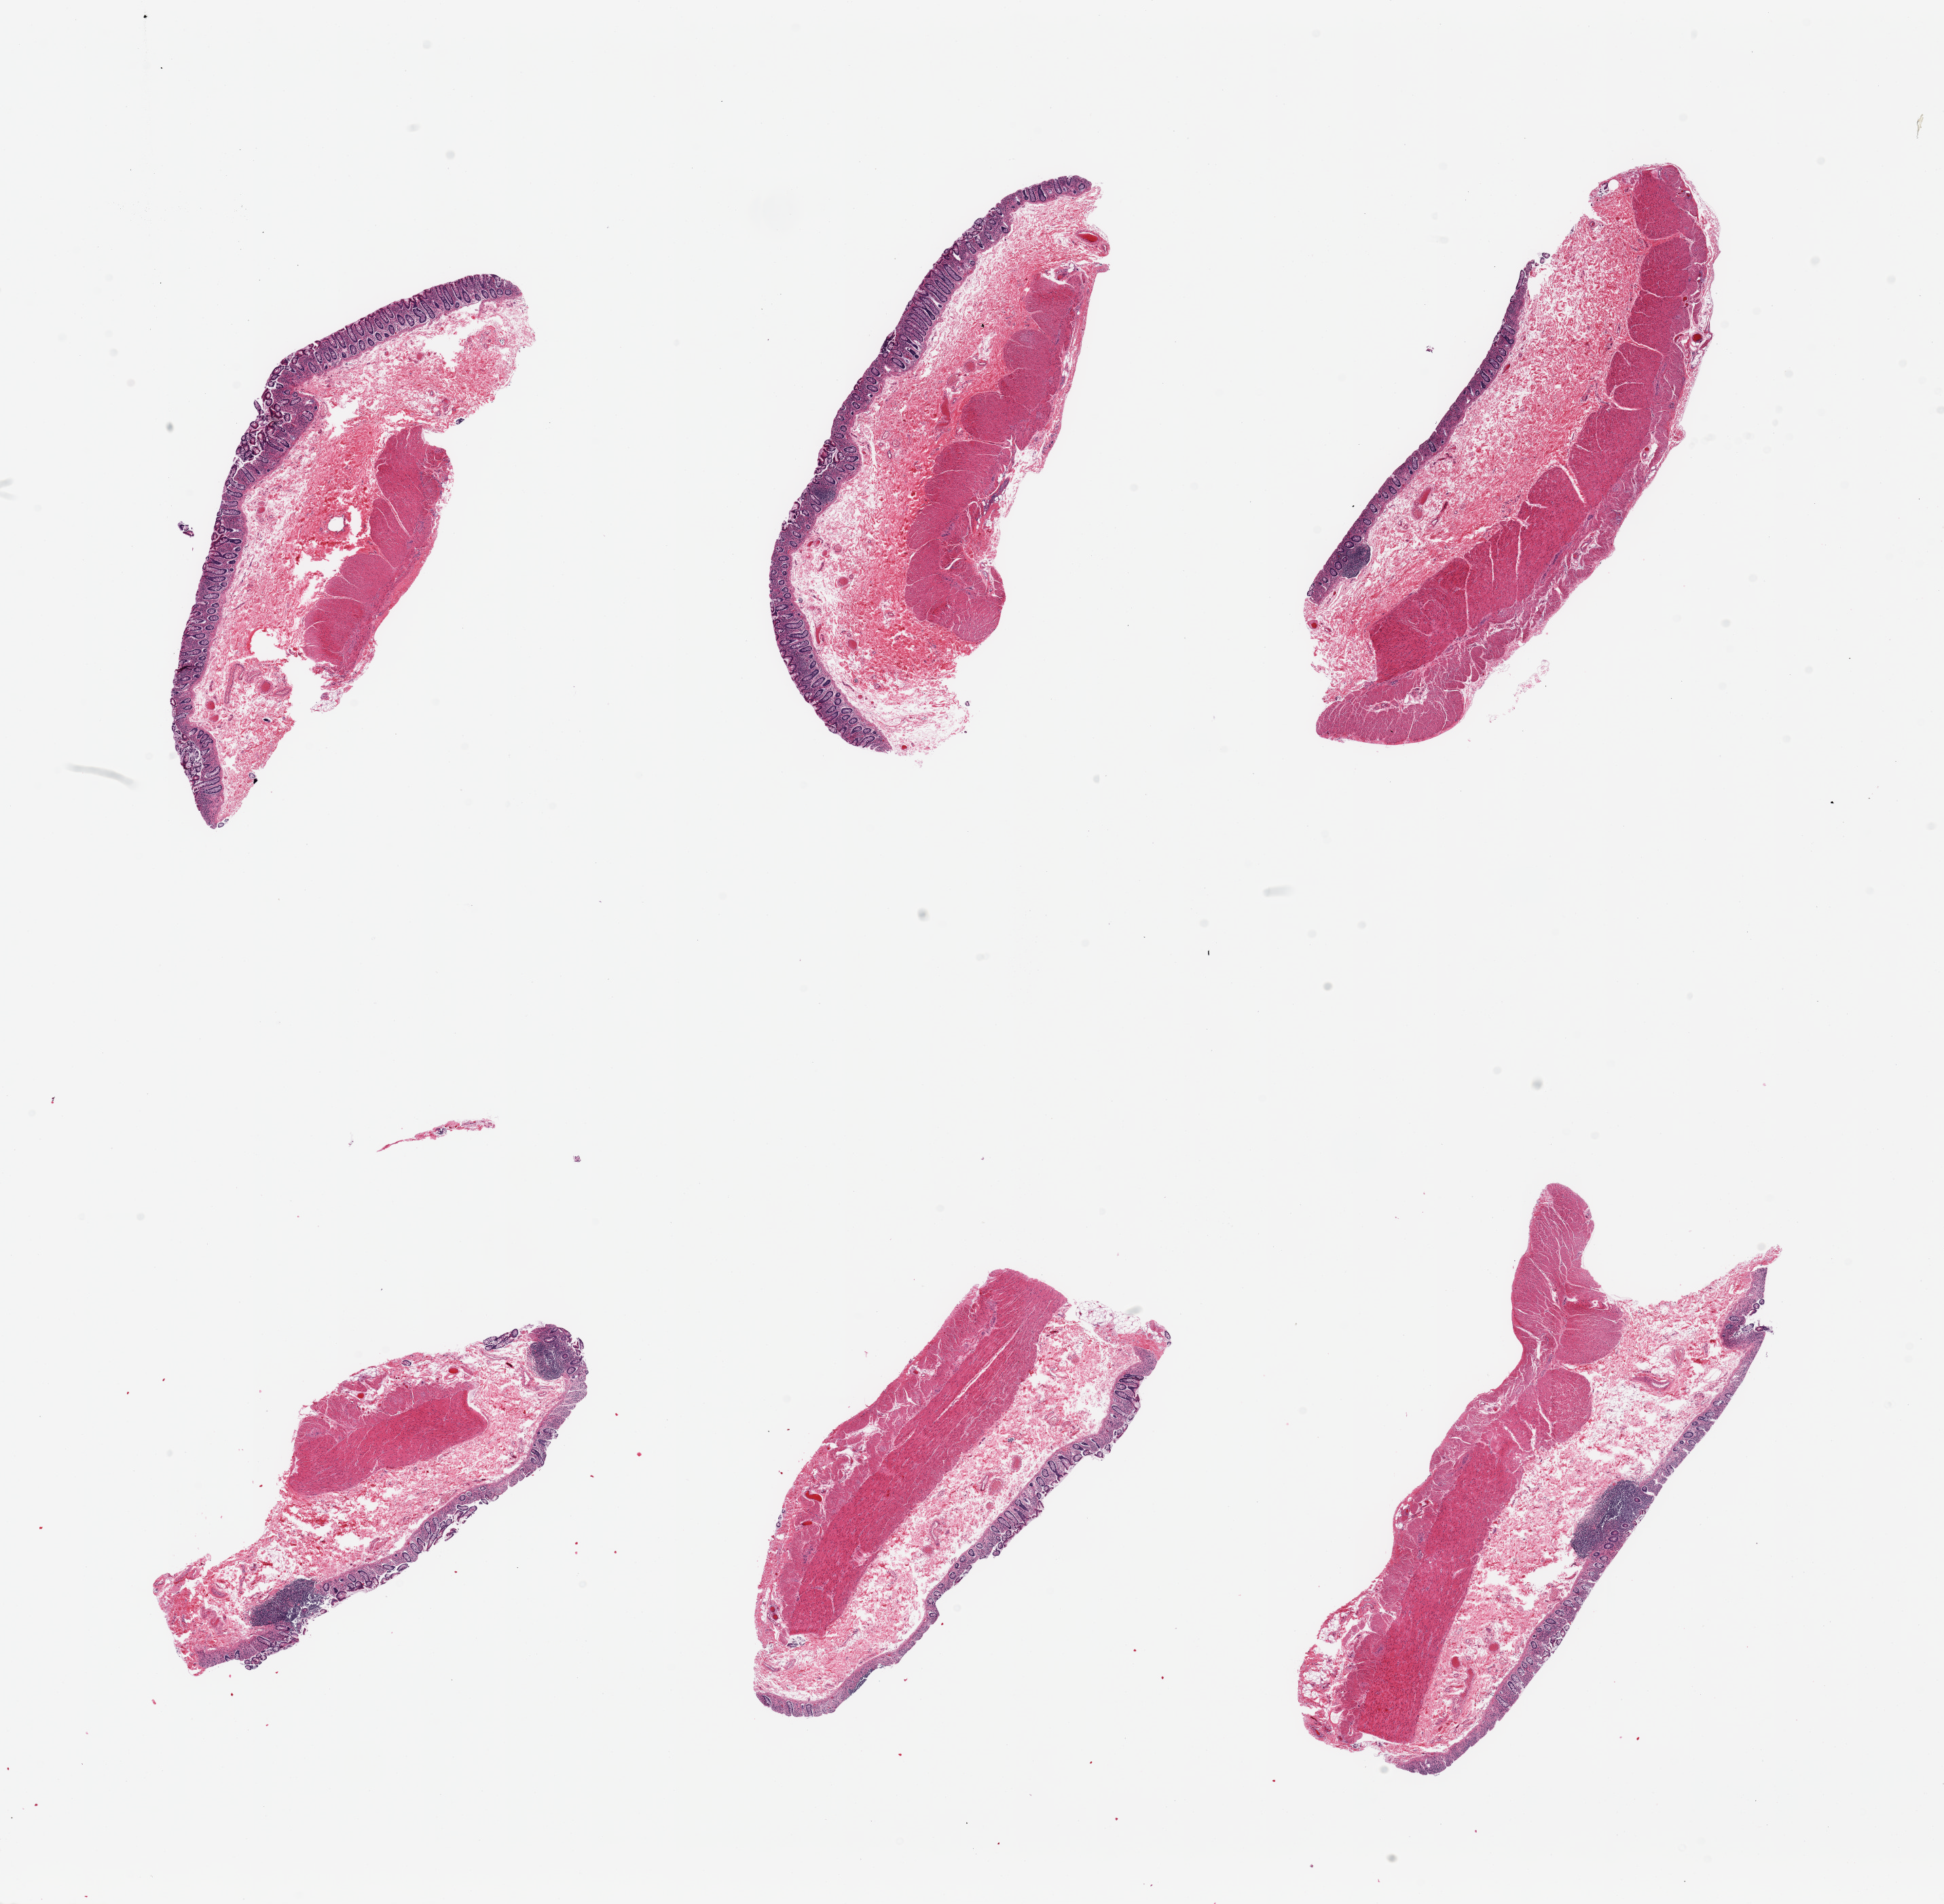
Hematoxylin and eosin (H&E) whole-slide image, brightfield — whole scanned area (about 22.6 x 22.2 mm, from a 20x scan) shown as a low-resolution overview. PAXgene-fixed, paraffin-embedded tissue. Sampled site (target tissue): transverse colon. Tissue donor sample. Male donor.
- review note (as recorded): 6 pieces; mucosa is main site of mild to moderate autolysis; muscle is intact